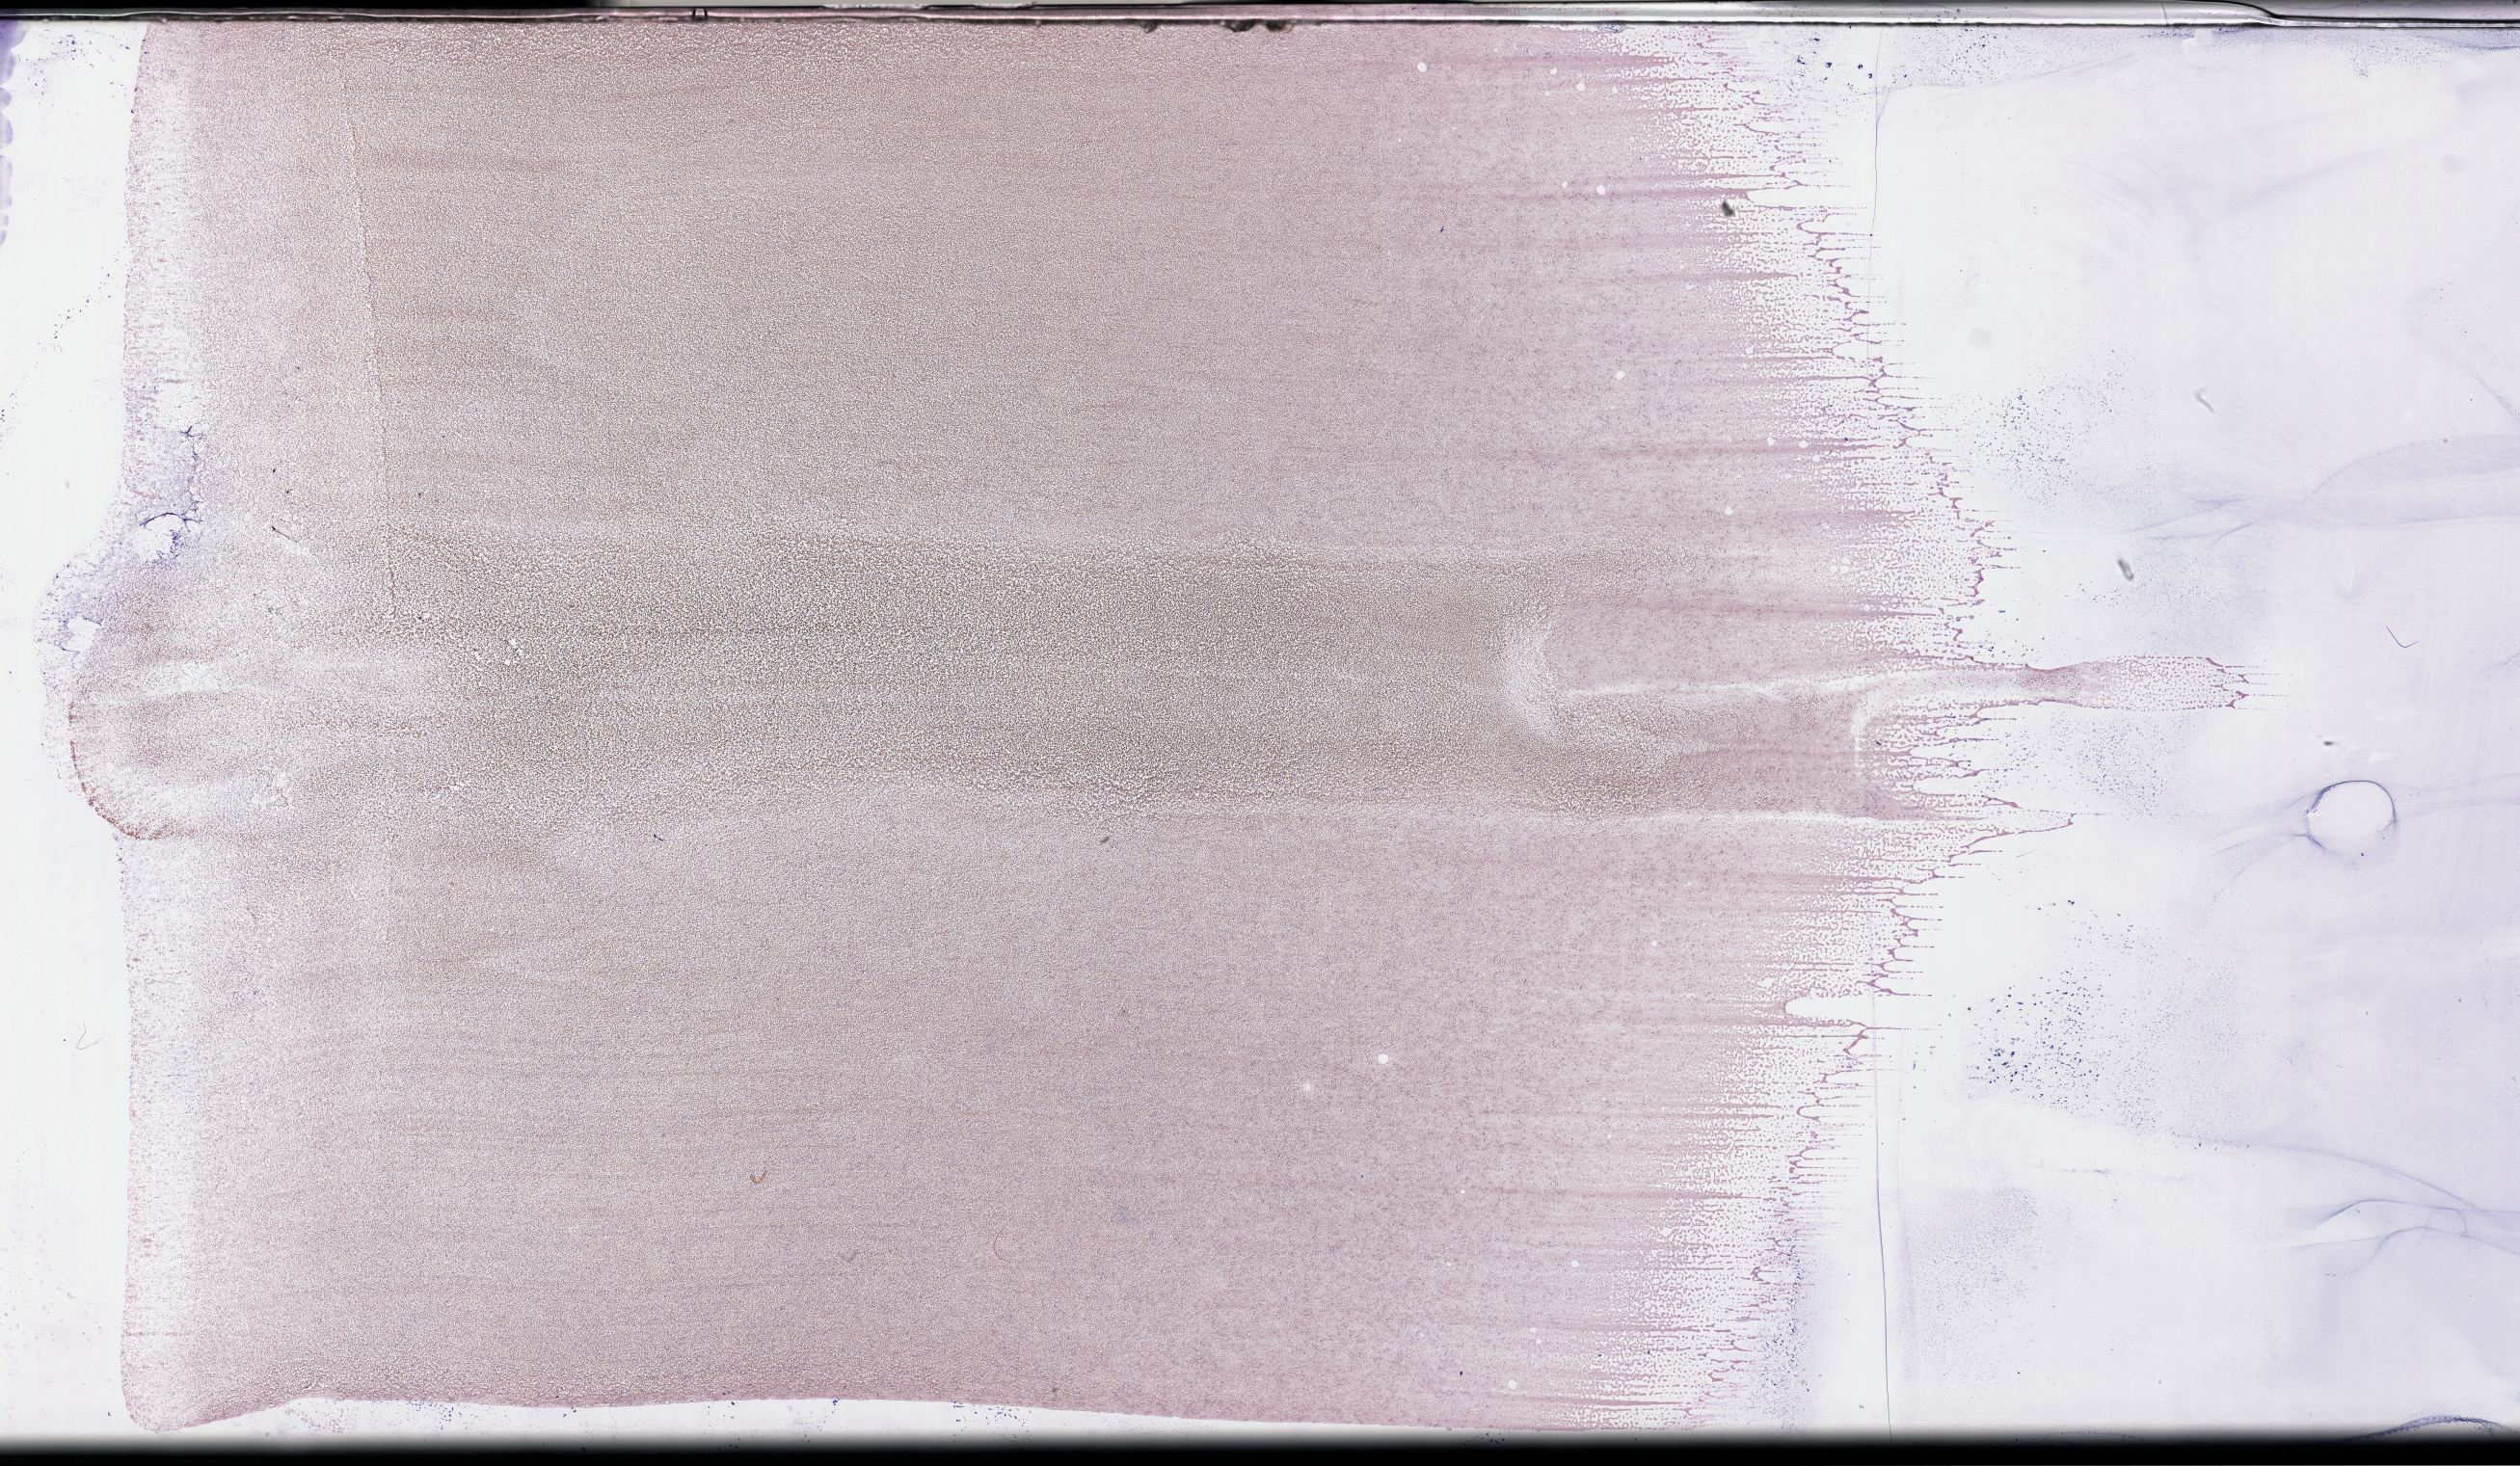
Wright-Giemsa-stained whole blood smear, whole-slide image — whole scanned area (about 42.2 x 24.6 mm) shown as a low-resolution overview, EDTA-anticoagulated smear, collected at baseline (before treatment). Female patient.
Patient diagnosis: Acute Myeloid Leukemia Not Otherwise Specified.